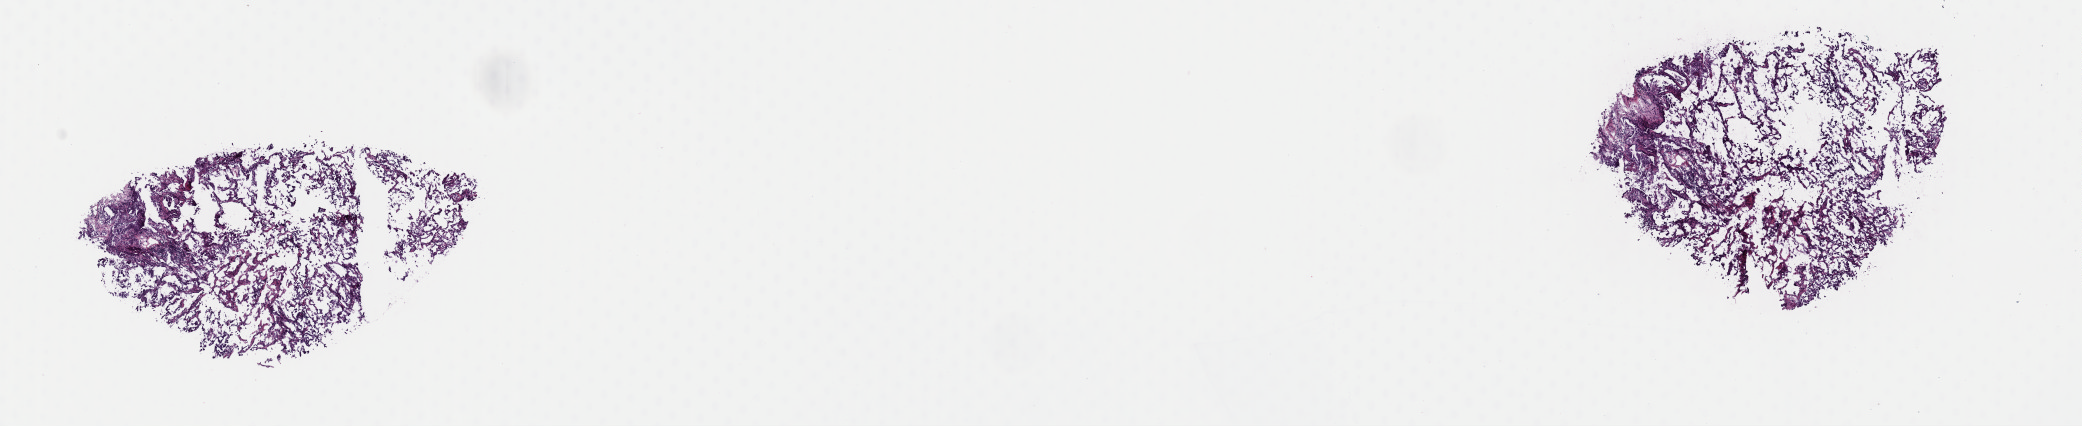
H&E-stained whole-slide image — low-resolution overview of the scanned area, about 16.4 x 3.4 mm (slide scanned at 40x). Frozen section. Lung, primary tumour sample. Female, age 77 years at initial diagnosis. Composition of this section per pathologist review: tumour cells 100%, tumour nuclei 65%, normal cells 0%, stromal cells 0%, necrosis 0%. Inflammatory infiltration, as recorded: lymphocyte infiltration 4%, monocyte infiltration 2%, neutrophil infiltration 0%.
- AJCC pathologic stage: IA (7th edition)
- pathologic diagnosis: Adenocarcinoma, NOS (upper lobe, lung)
- laterality: left